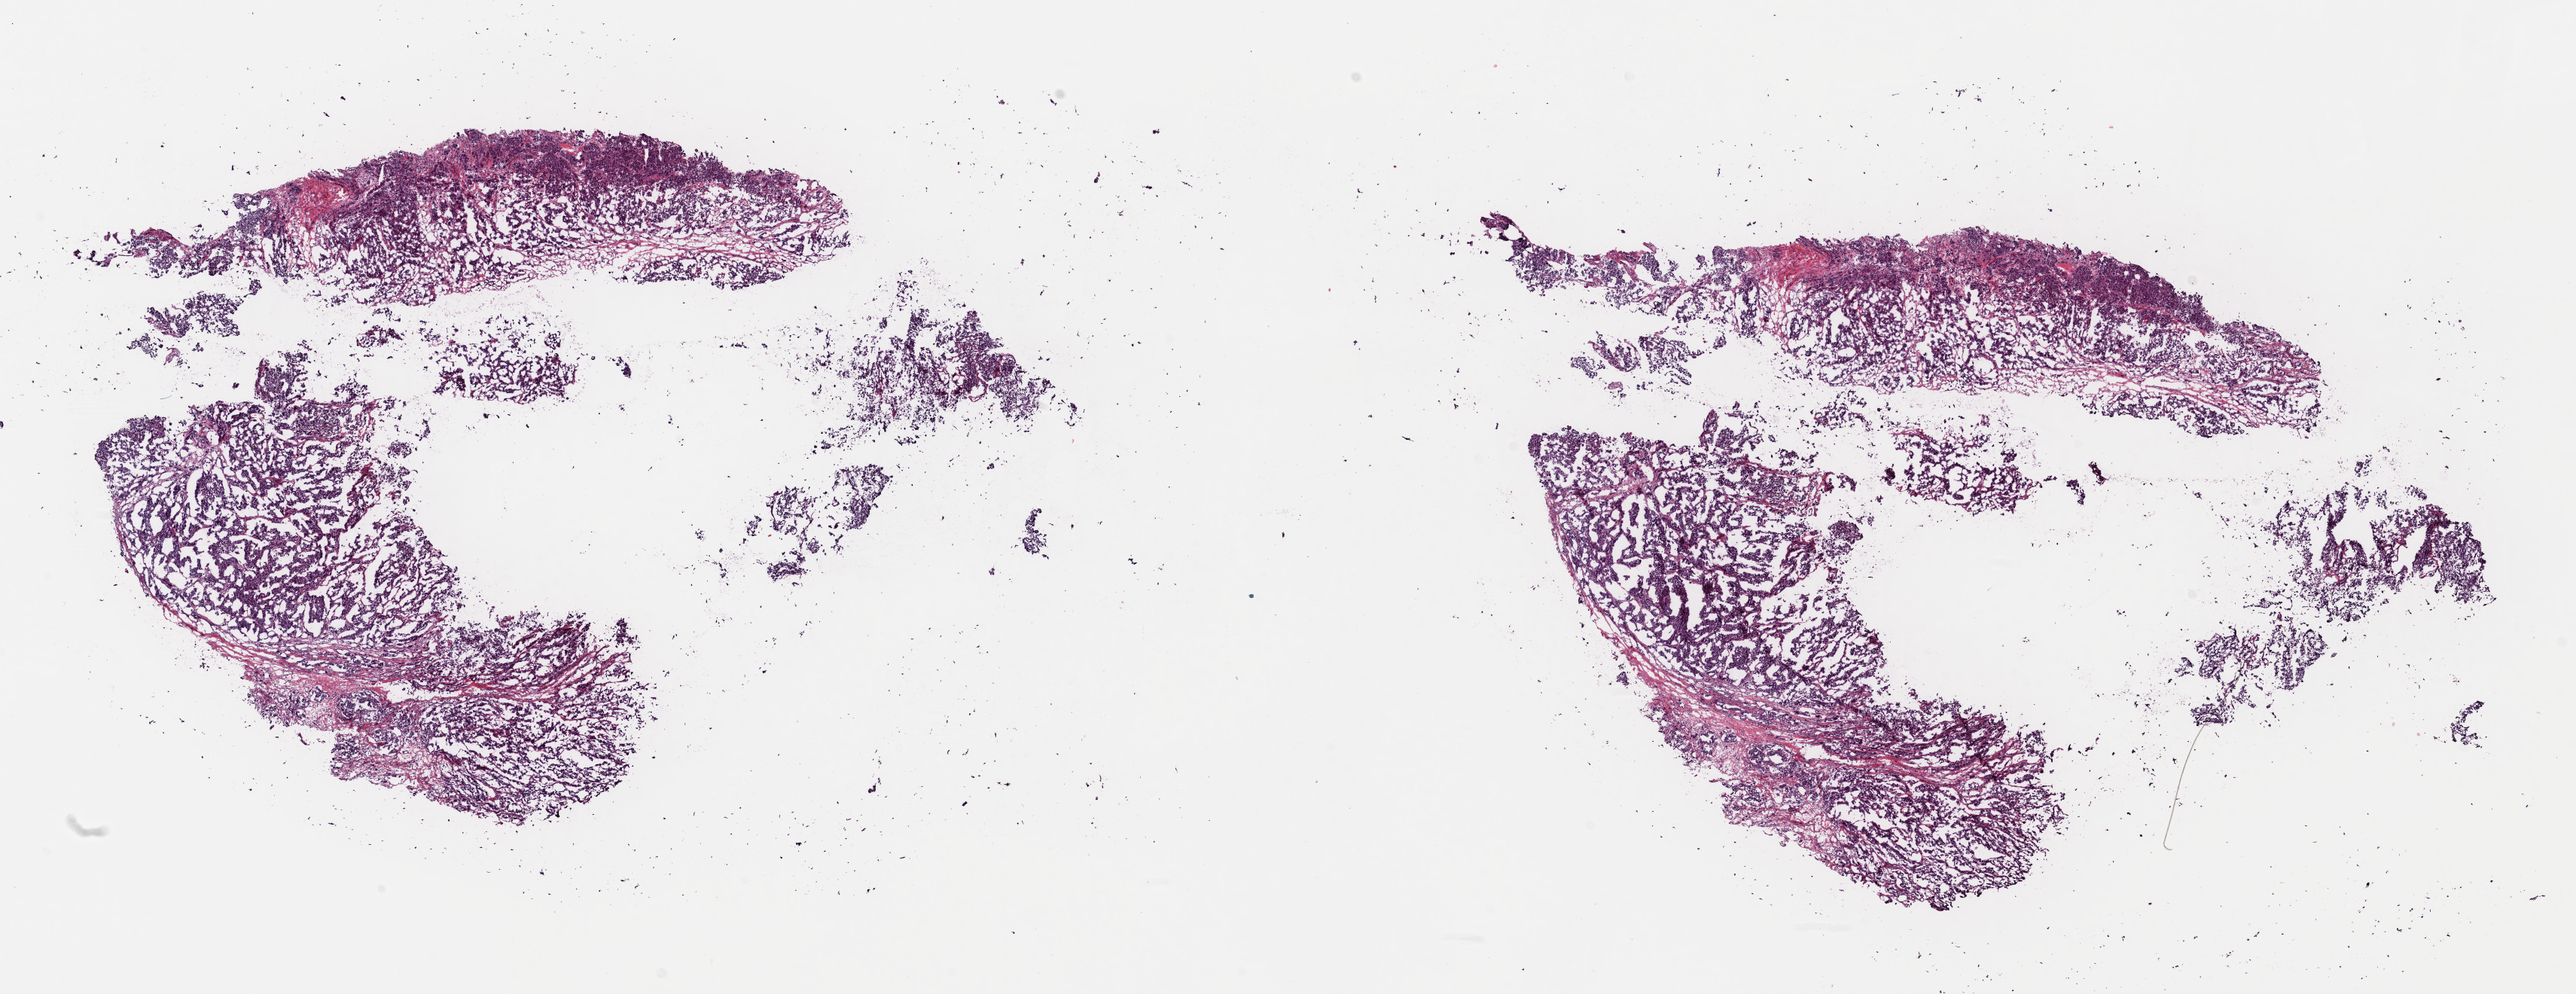
H&E-stained whole-slide image, whole scanned area (about 26.9 x 10.4 mm) shown as a low-resolution overview, frozen section from the top of the tissue portion, metastatic tumour sample, sampled site: skin of trunk. Female, age 57 years at initial diagnosis. Slide review estimates, as recorded: tumour cells 85%, tumour nuclei 85%, normal cells 0%, stromal cells 14%, necrosis 1%. Inflammatory infiltration, as recorded: lymphocyte infiltration 2%, monocyte infiltration 1%, neutrophil infiltration 1%.
This section: metastatic tumour tissue. Patient diagnosis: Malignant melanoma, NOS.